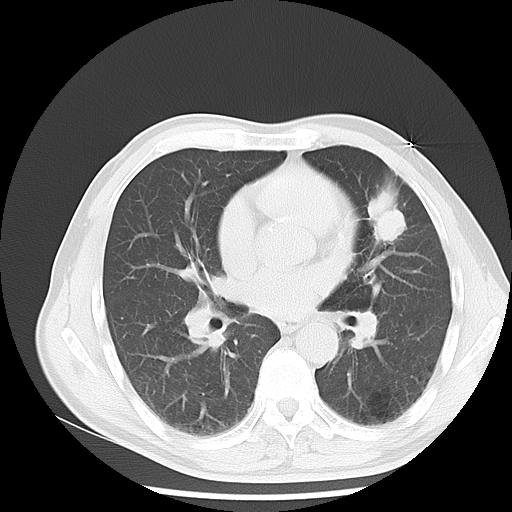
Chest CT, one axial slice; reconstruction kernel LUNG; 120 kVp; lung window (W 1500 / L -600 HU); 5 mm slice thickness; 512 × 512 image matrix, field of view 350 × 350 mm. Patient: male, 54 years. Case-level facts recorded for this patient, not image findings: clinical TNM (as recorded): T1c N0 M0.
Annotated regions visible in this slice (rectangle marked by the reading radiologist):
- lung tumour (recorded histology: adenocarcinoma): box from (x=367, y=190) to (x=410, y=245) px